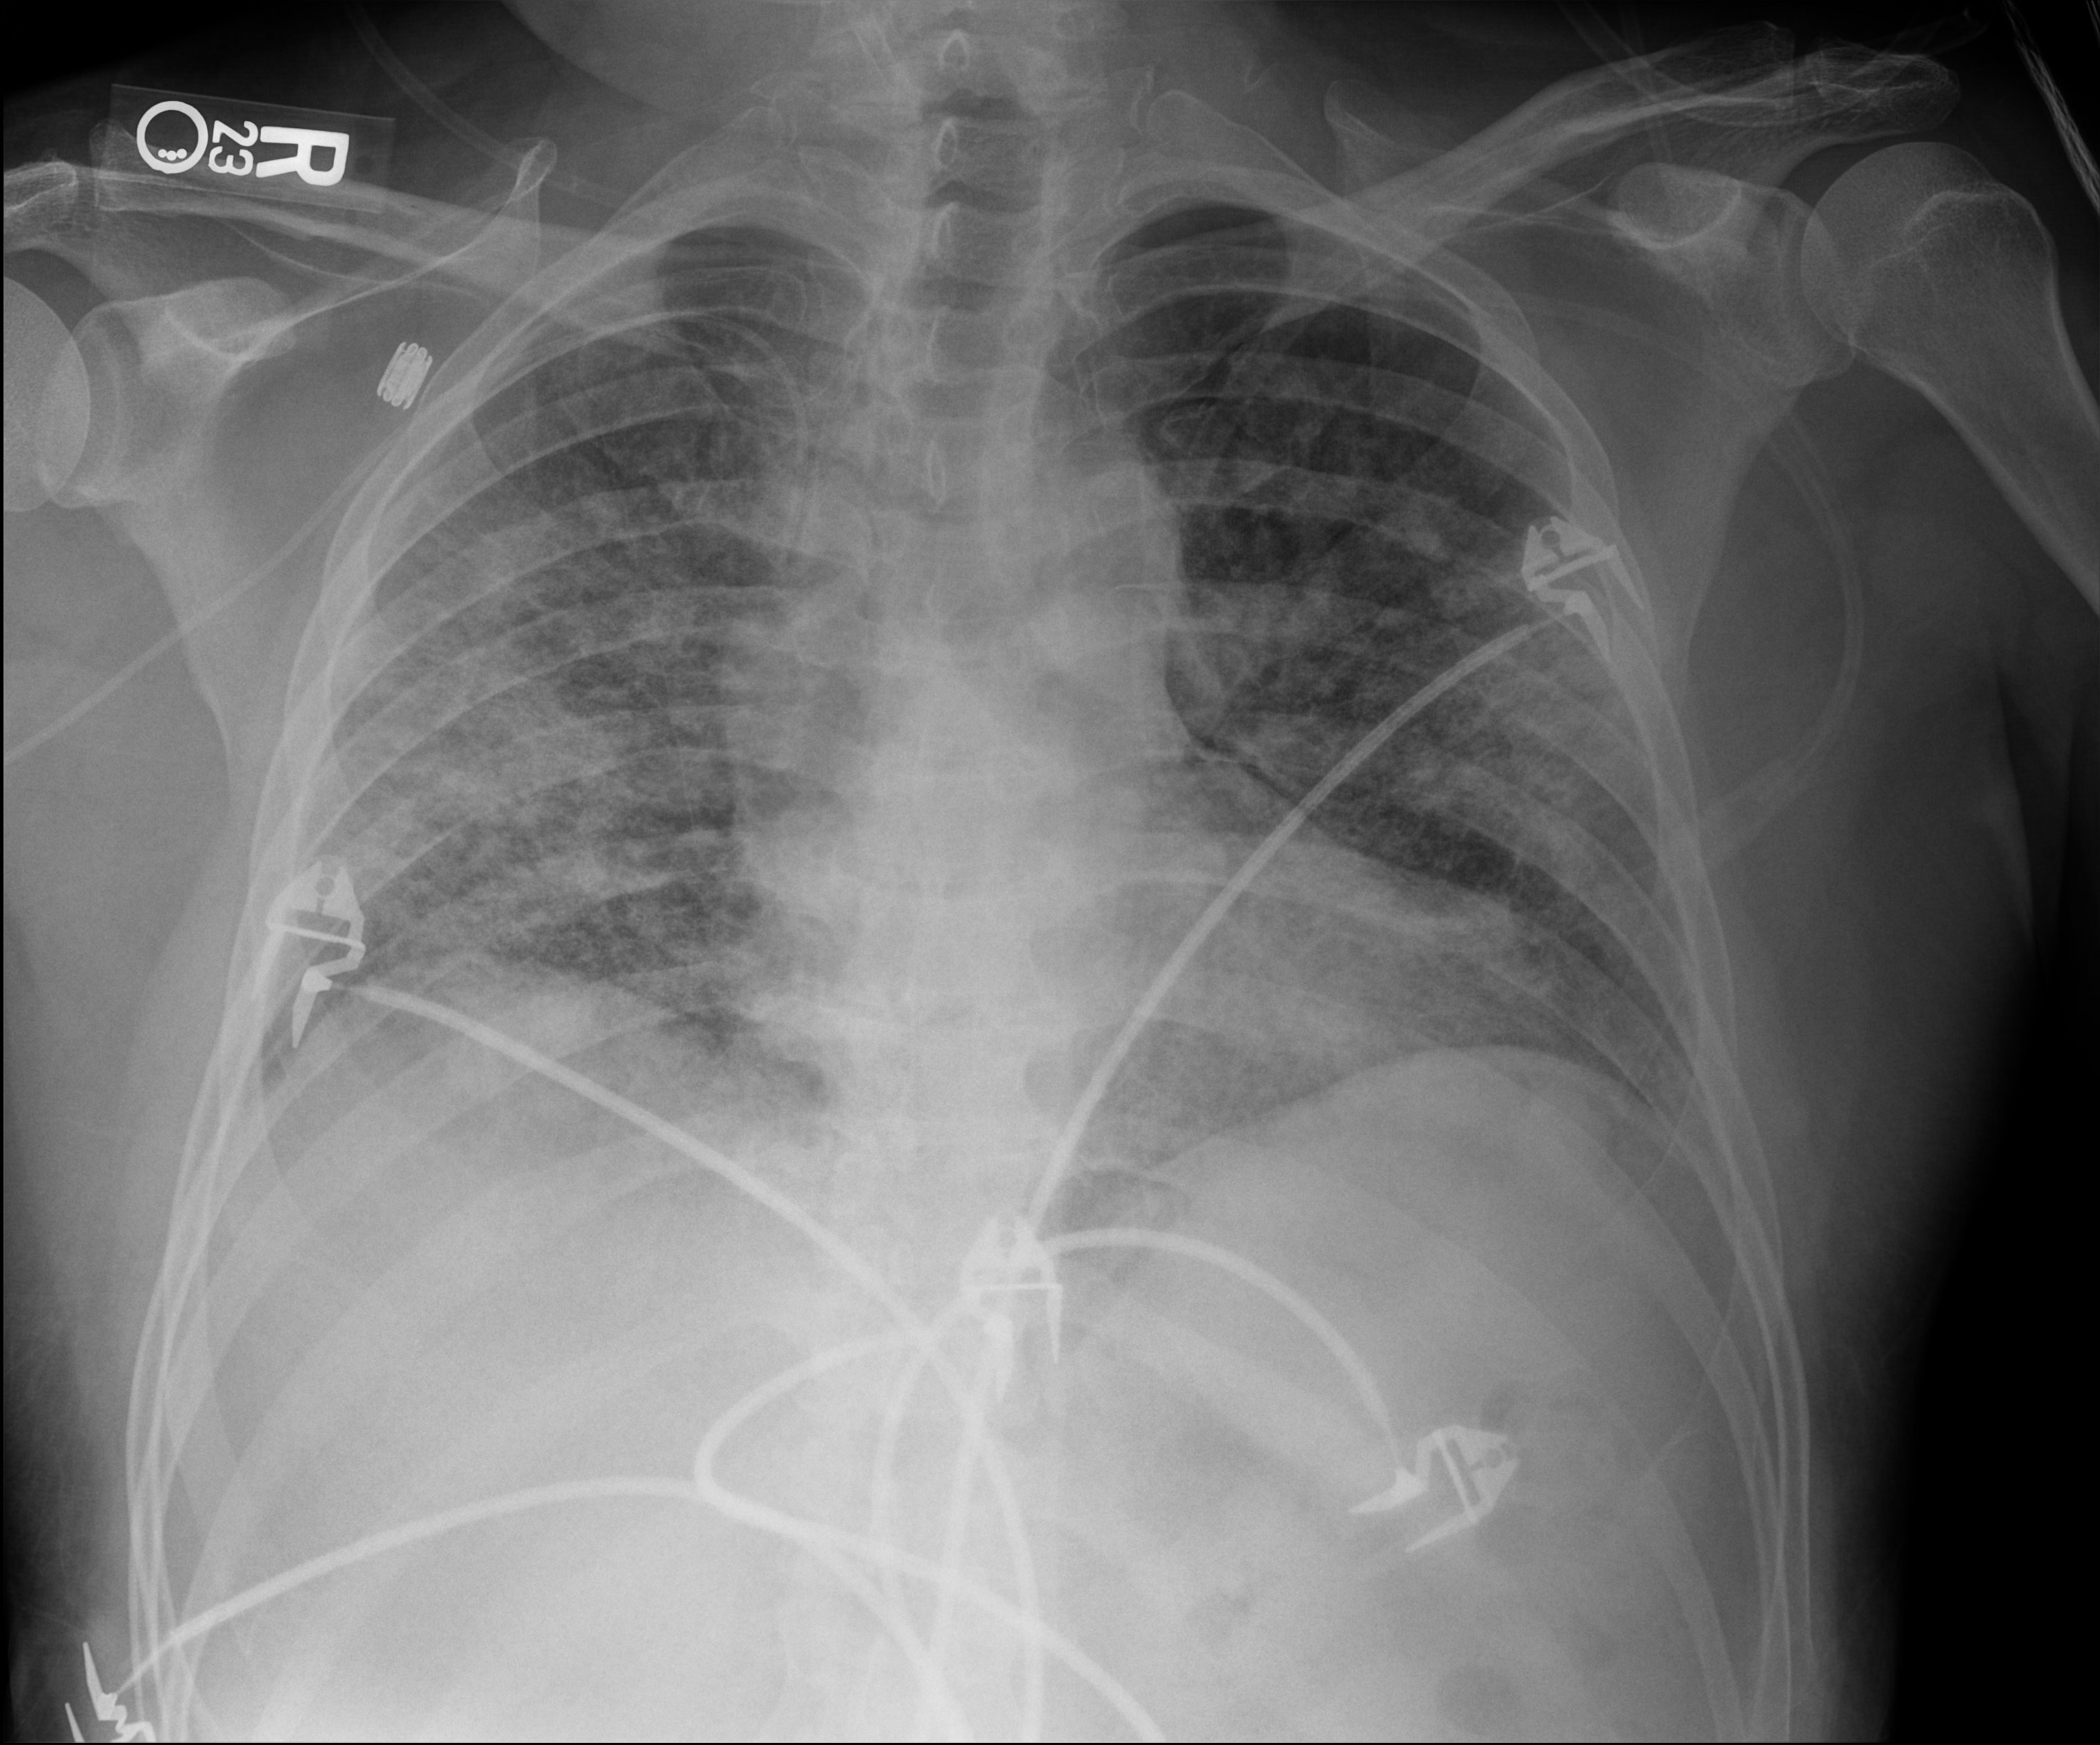
Chest X-ray, anteroposterior (AP) projection. Patient hospitalised with COVID-19; male, aged 18–59 years.
Hospital-stay facts (about this admission, not read from this image; timing relative to this image not recorded): diabetes (admission record): no.